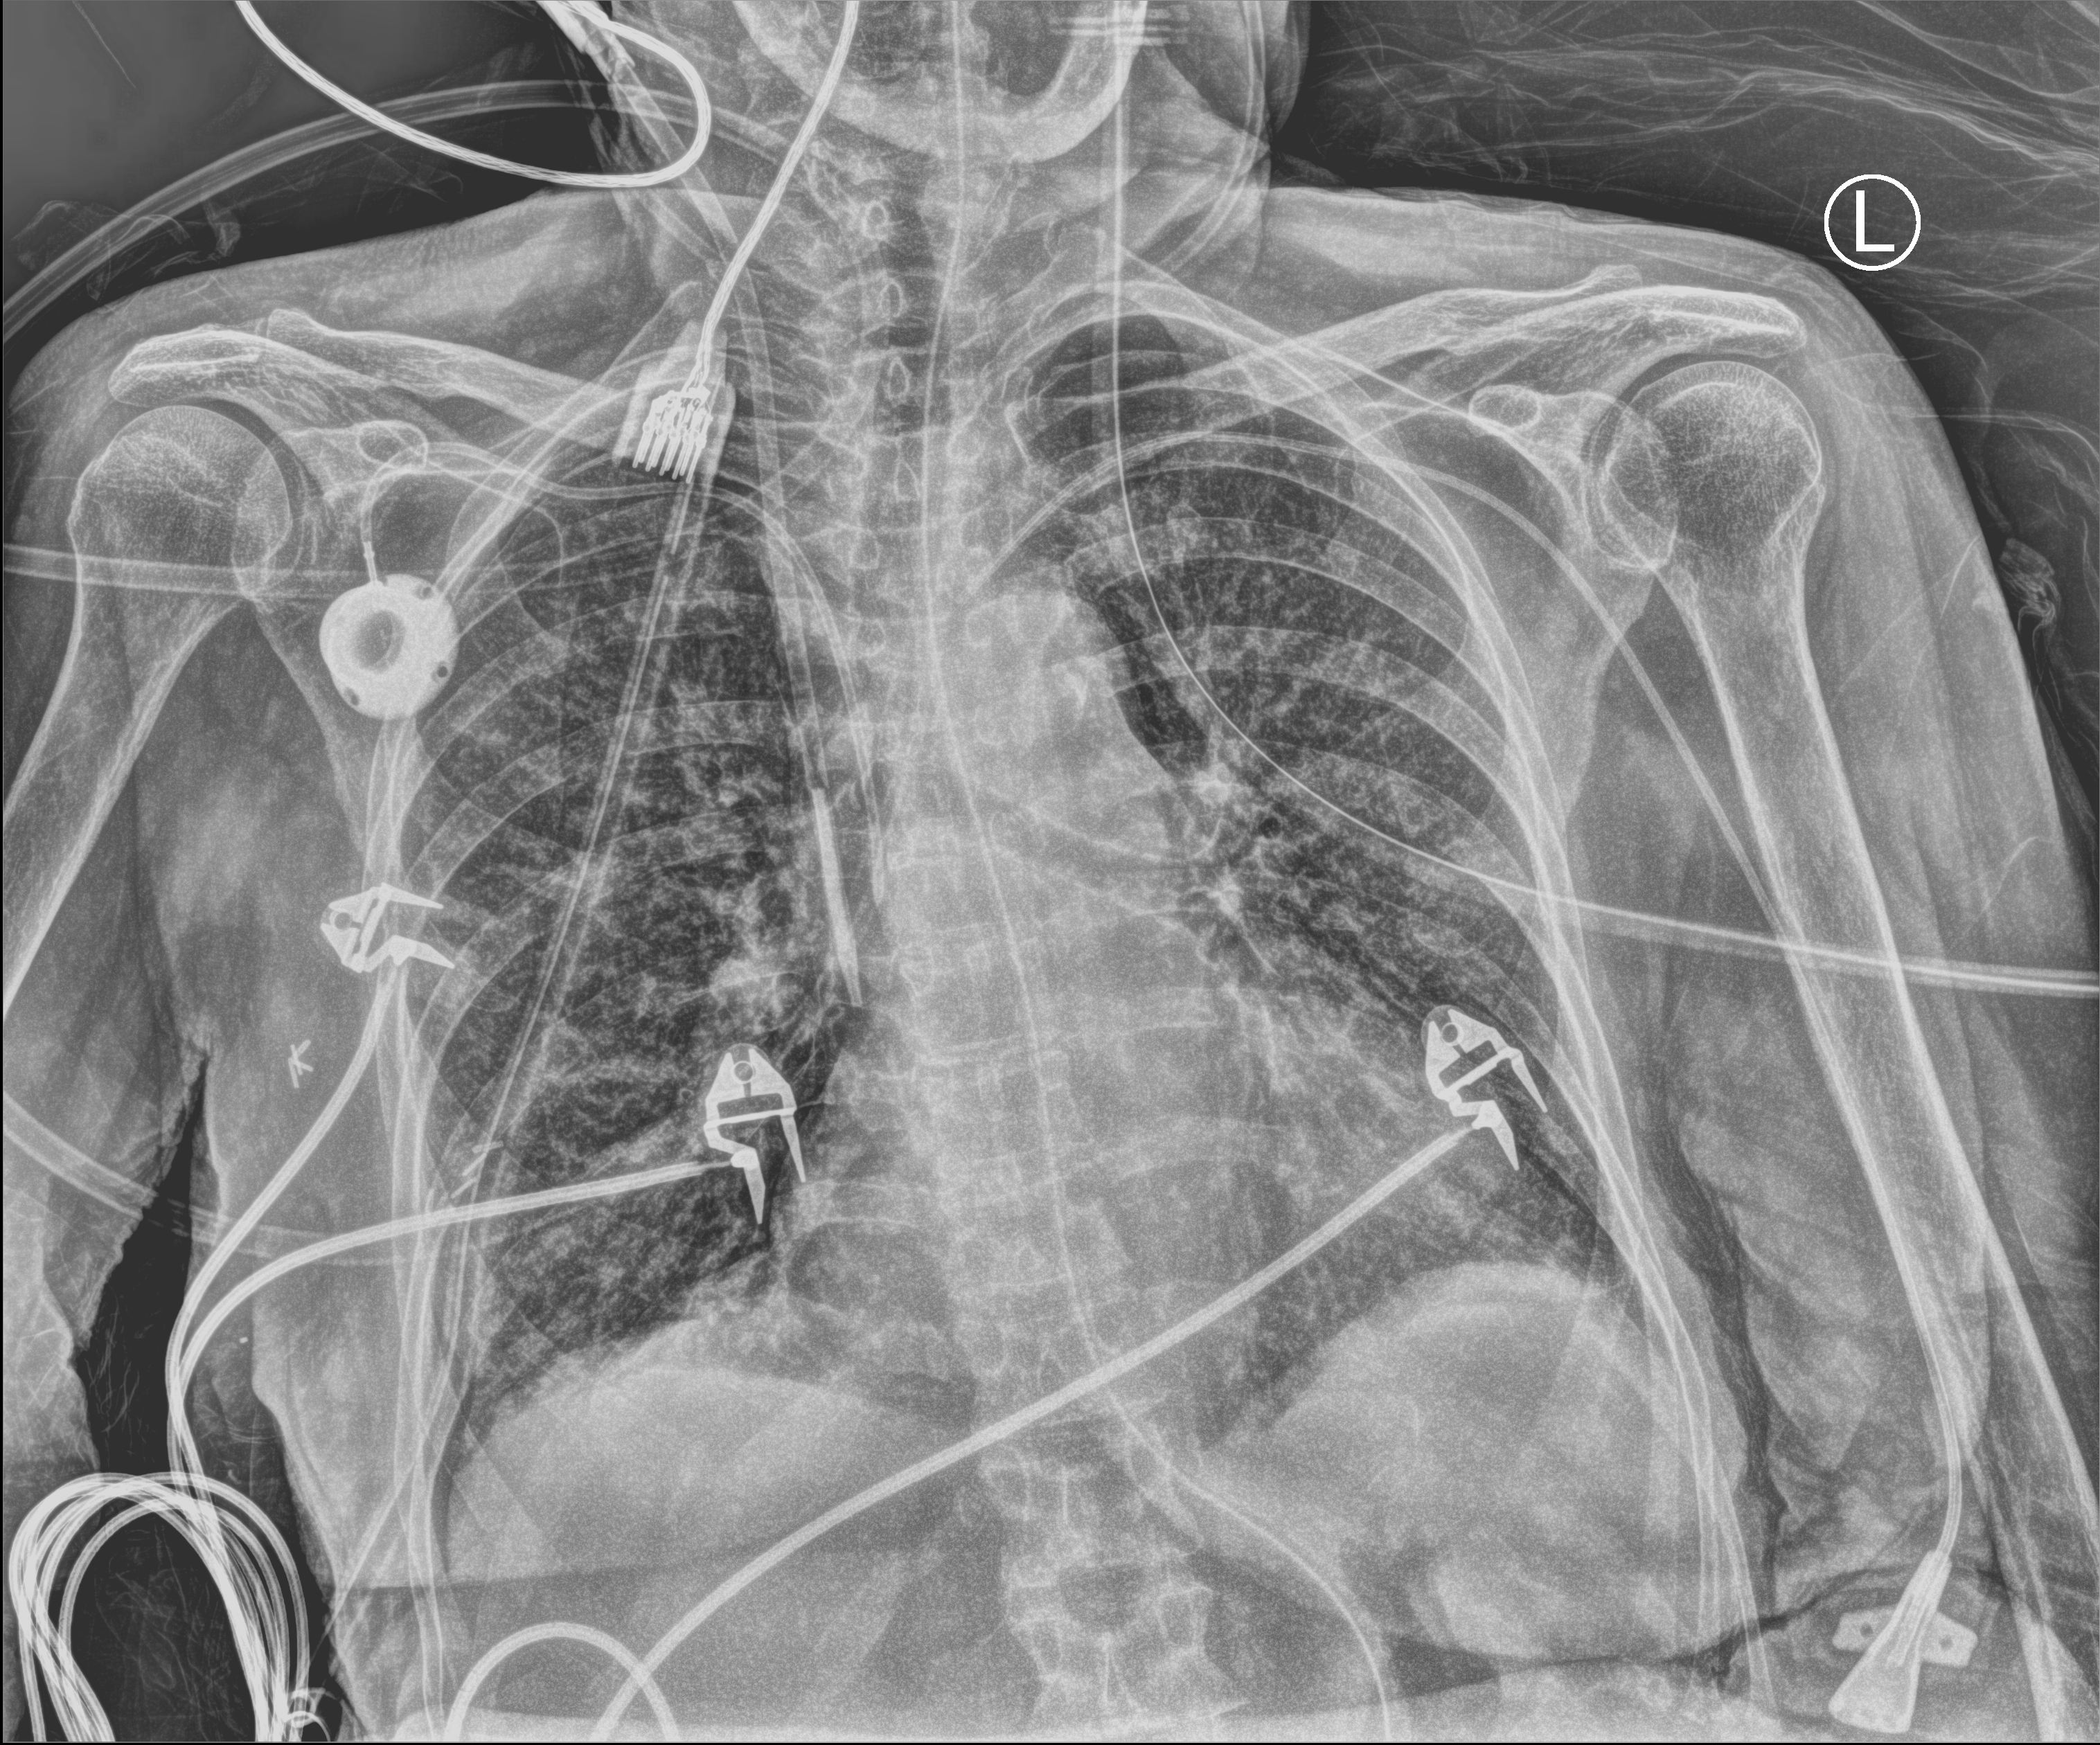
Chest X-ray (portable); anteroposterior (AP) projection. Female patient hospitalised with COVID-19, age 60–74 years.
Hospital-stay facts (about this admission, not read from this image; timing relative to this image not recorded): hypertension (admission record): yes; COPD (admission record): no; admitted to intensive care during this hospital stay: yes.